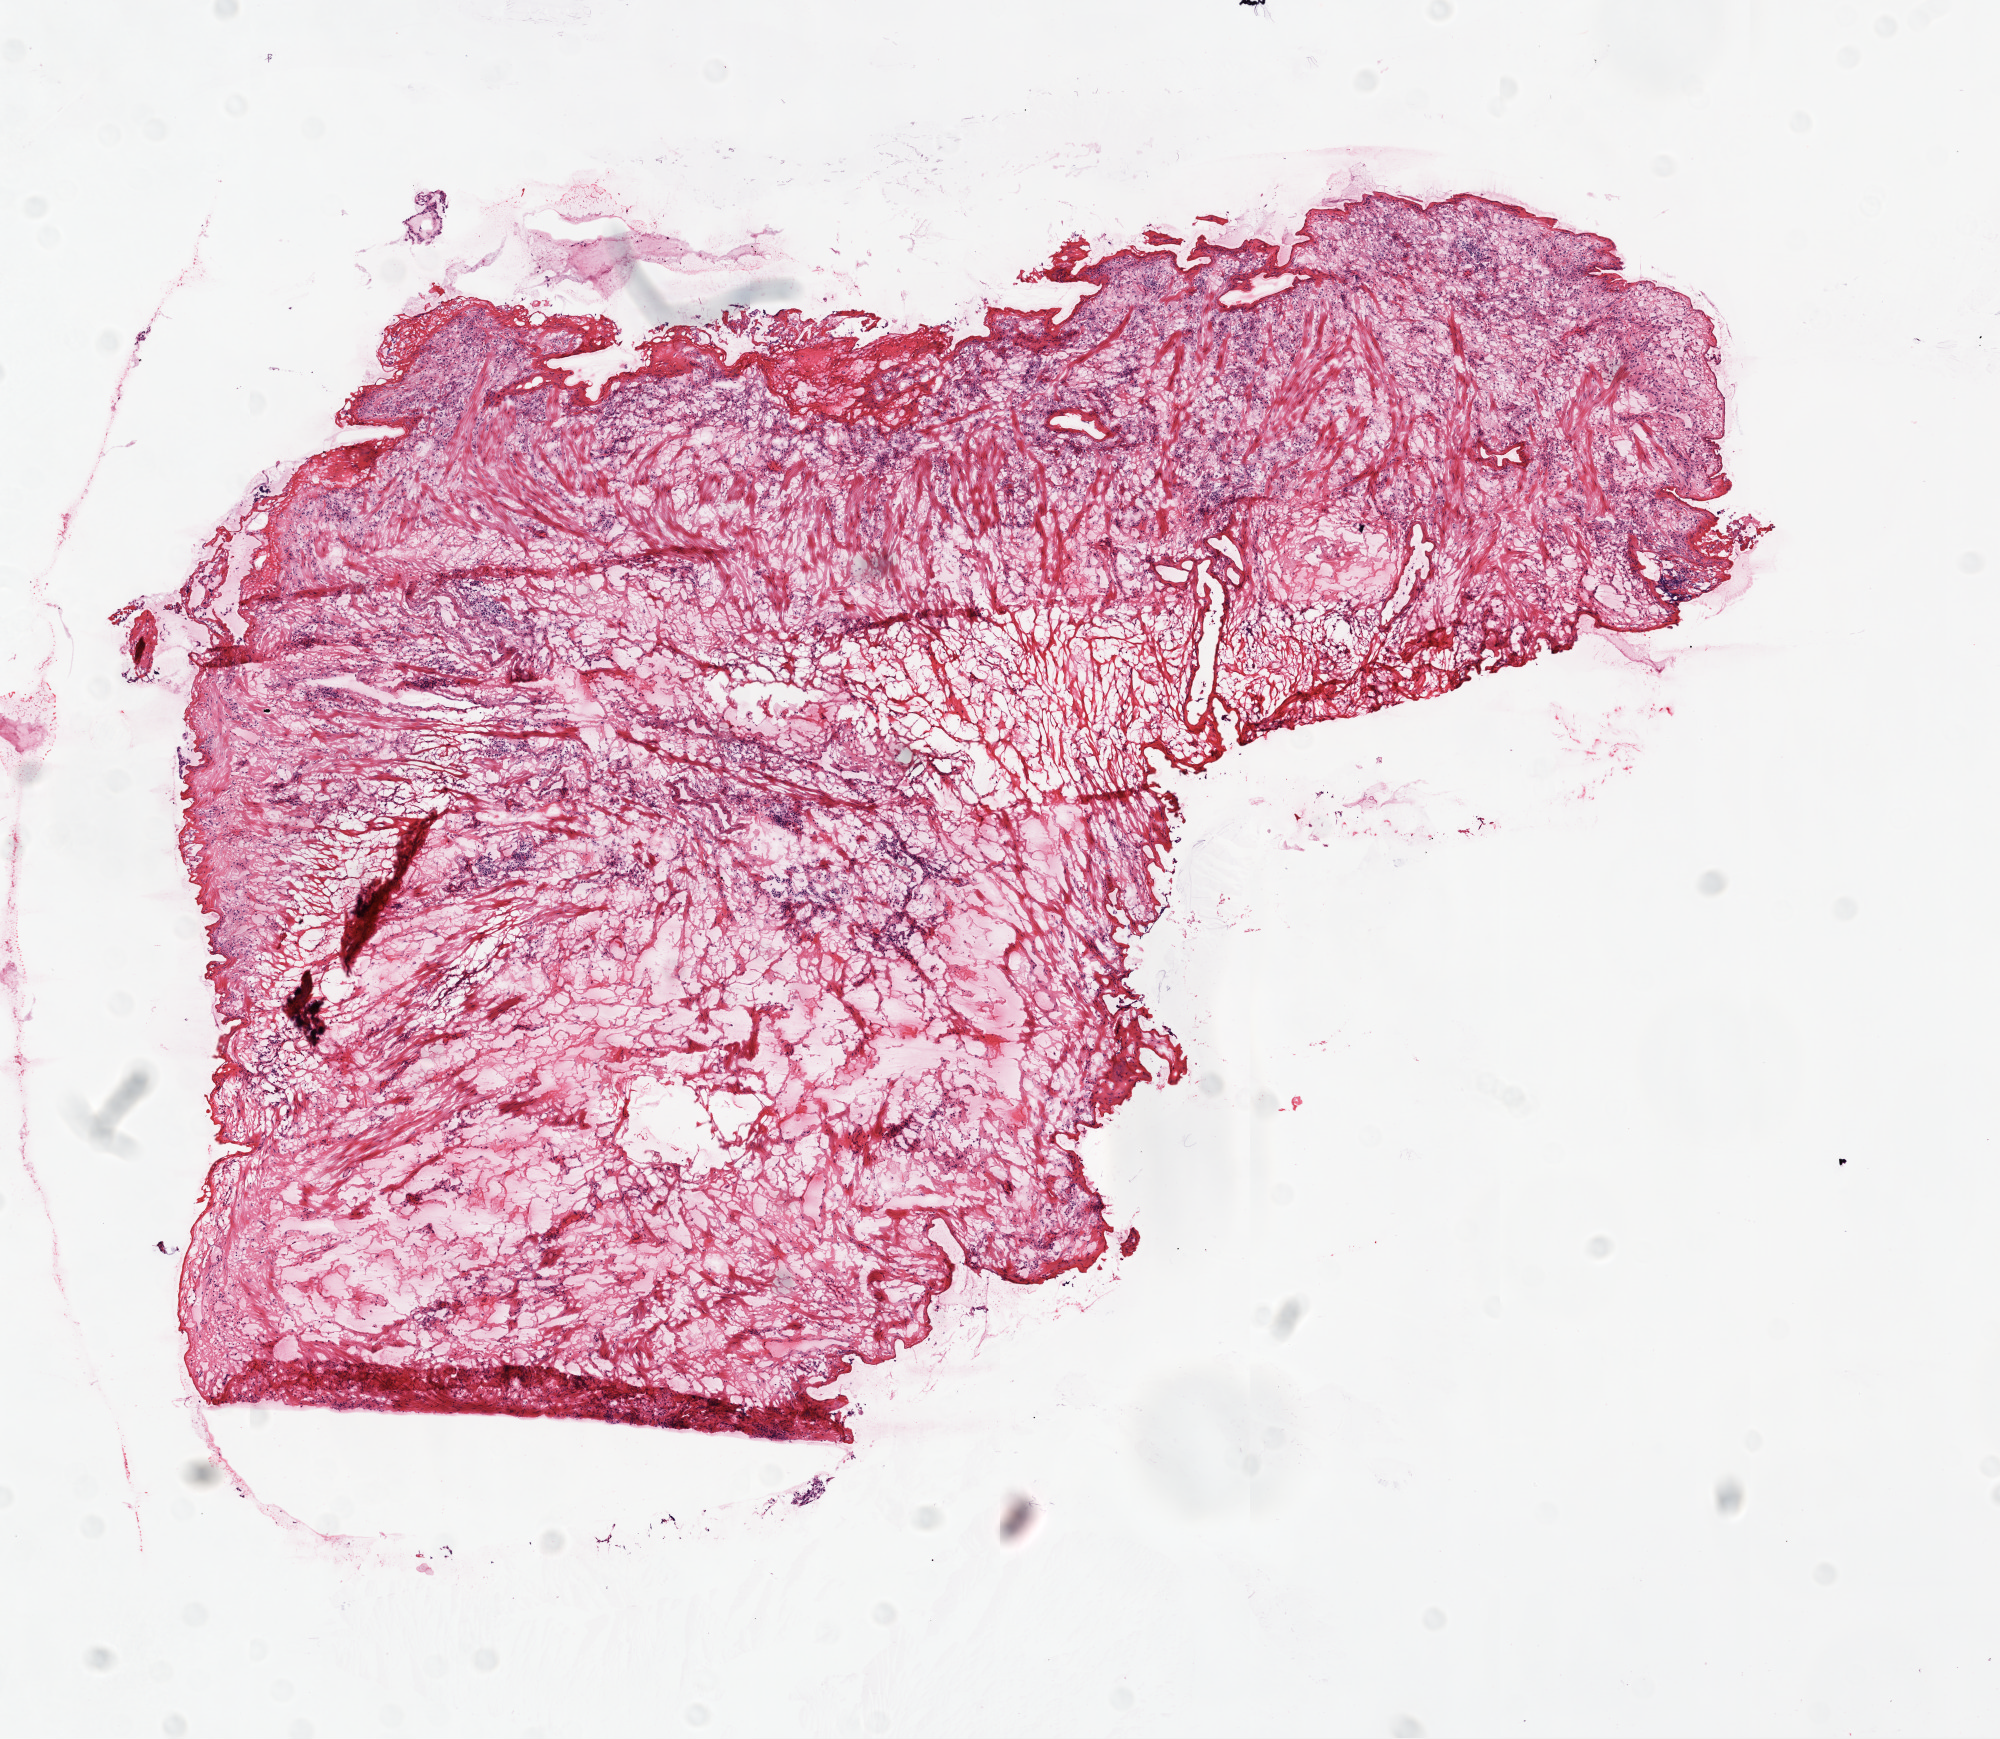
H&E-stained whole-slide image, shown as a low-resolution overview of the whole scanned area (about 8.0 x 7.0 mm), frozen section from the top of the tissue portion, ovary, solid tissue normal (non-tumour tissue) sample. Female patient; age at initial diagnosis 58 years.
- this section: solid tissue normal (non-tumour) sample from the same patient
- patient diagnosis: Serous cystadenocarcinoma, NOS